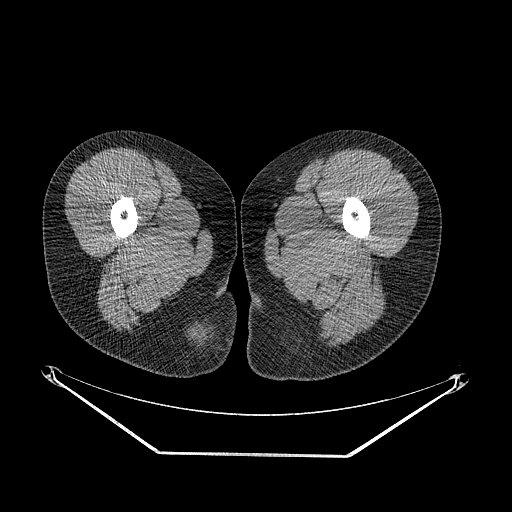
CT of an extremity soft-tissue mass (from a PET/CT study), one axial slice. Reconstruction kernel STANDARD. Soft-tissue window (W 400 / L 40 HU). 3.75 mm slice thickness. 512 × 512 image matrix. Female patient. Case-level facts recorded for this patient, not image findings: histological type: epithelioid sarcoma; grade: intermediate; site of the primary tumour: right buttock.
Annotated regions visible in this slice (expert contour drawn on MRI and transferred to this co-registered scan by the dataset authors):
- gross tumour volume including surrounding oedema: bounding box [x1, y1, x2, y2] px = [178, 317, 234, 384]
- gross tumour volume (mass): [189, 326, 211, 346]